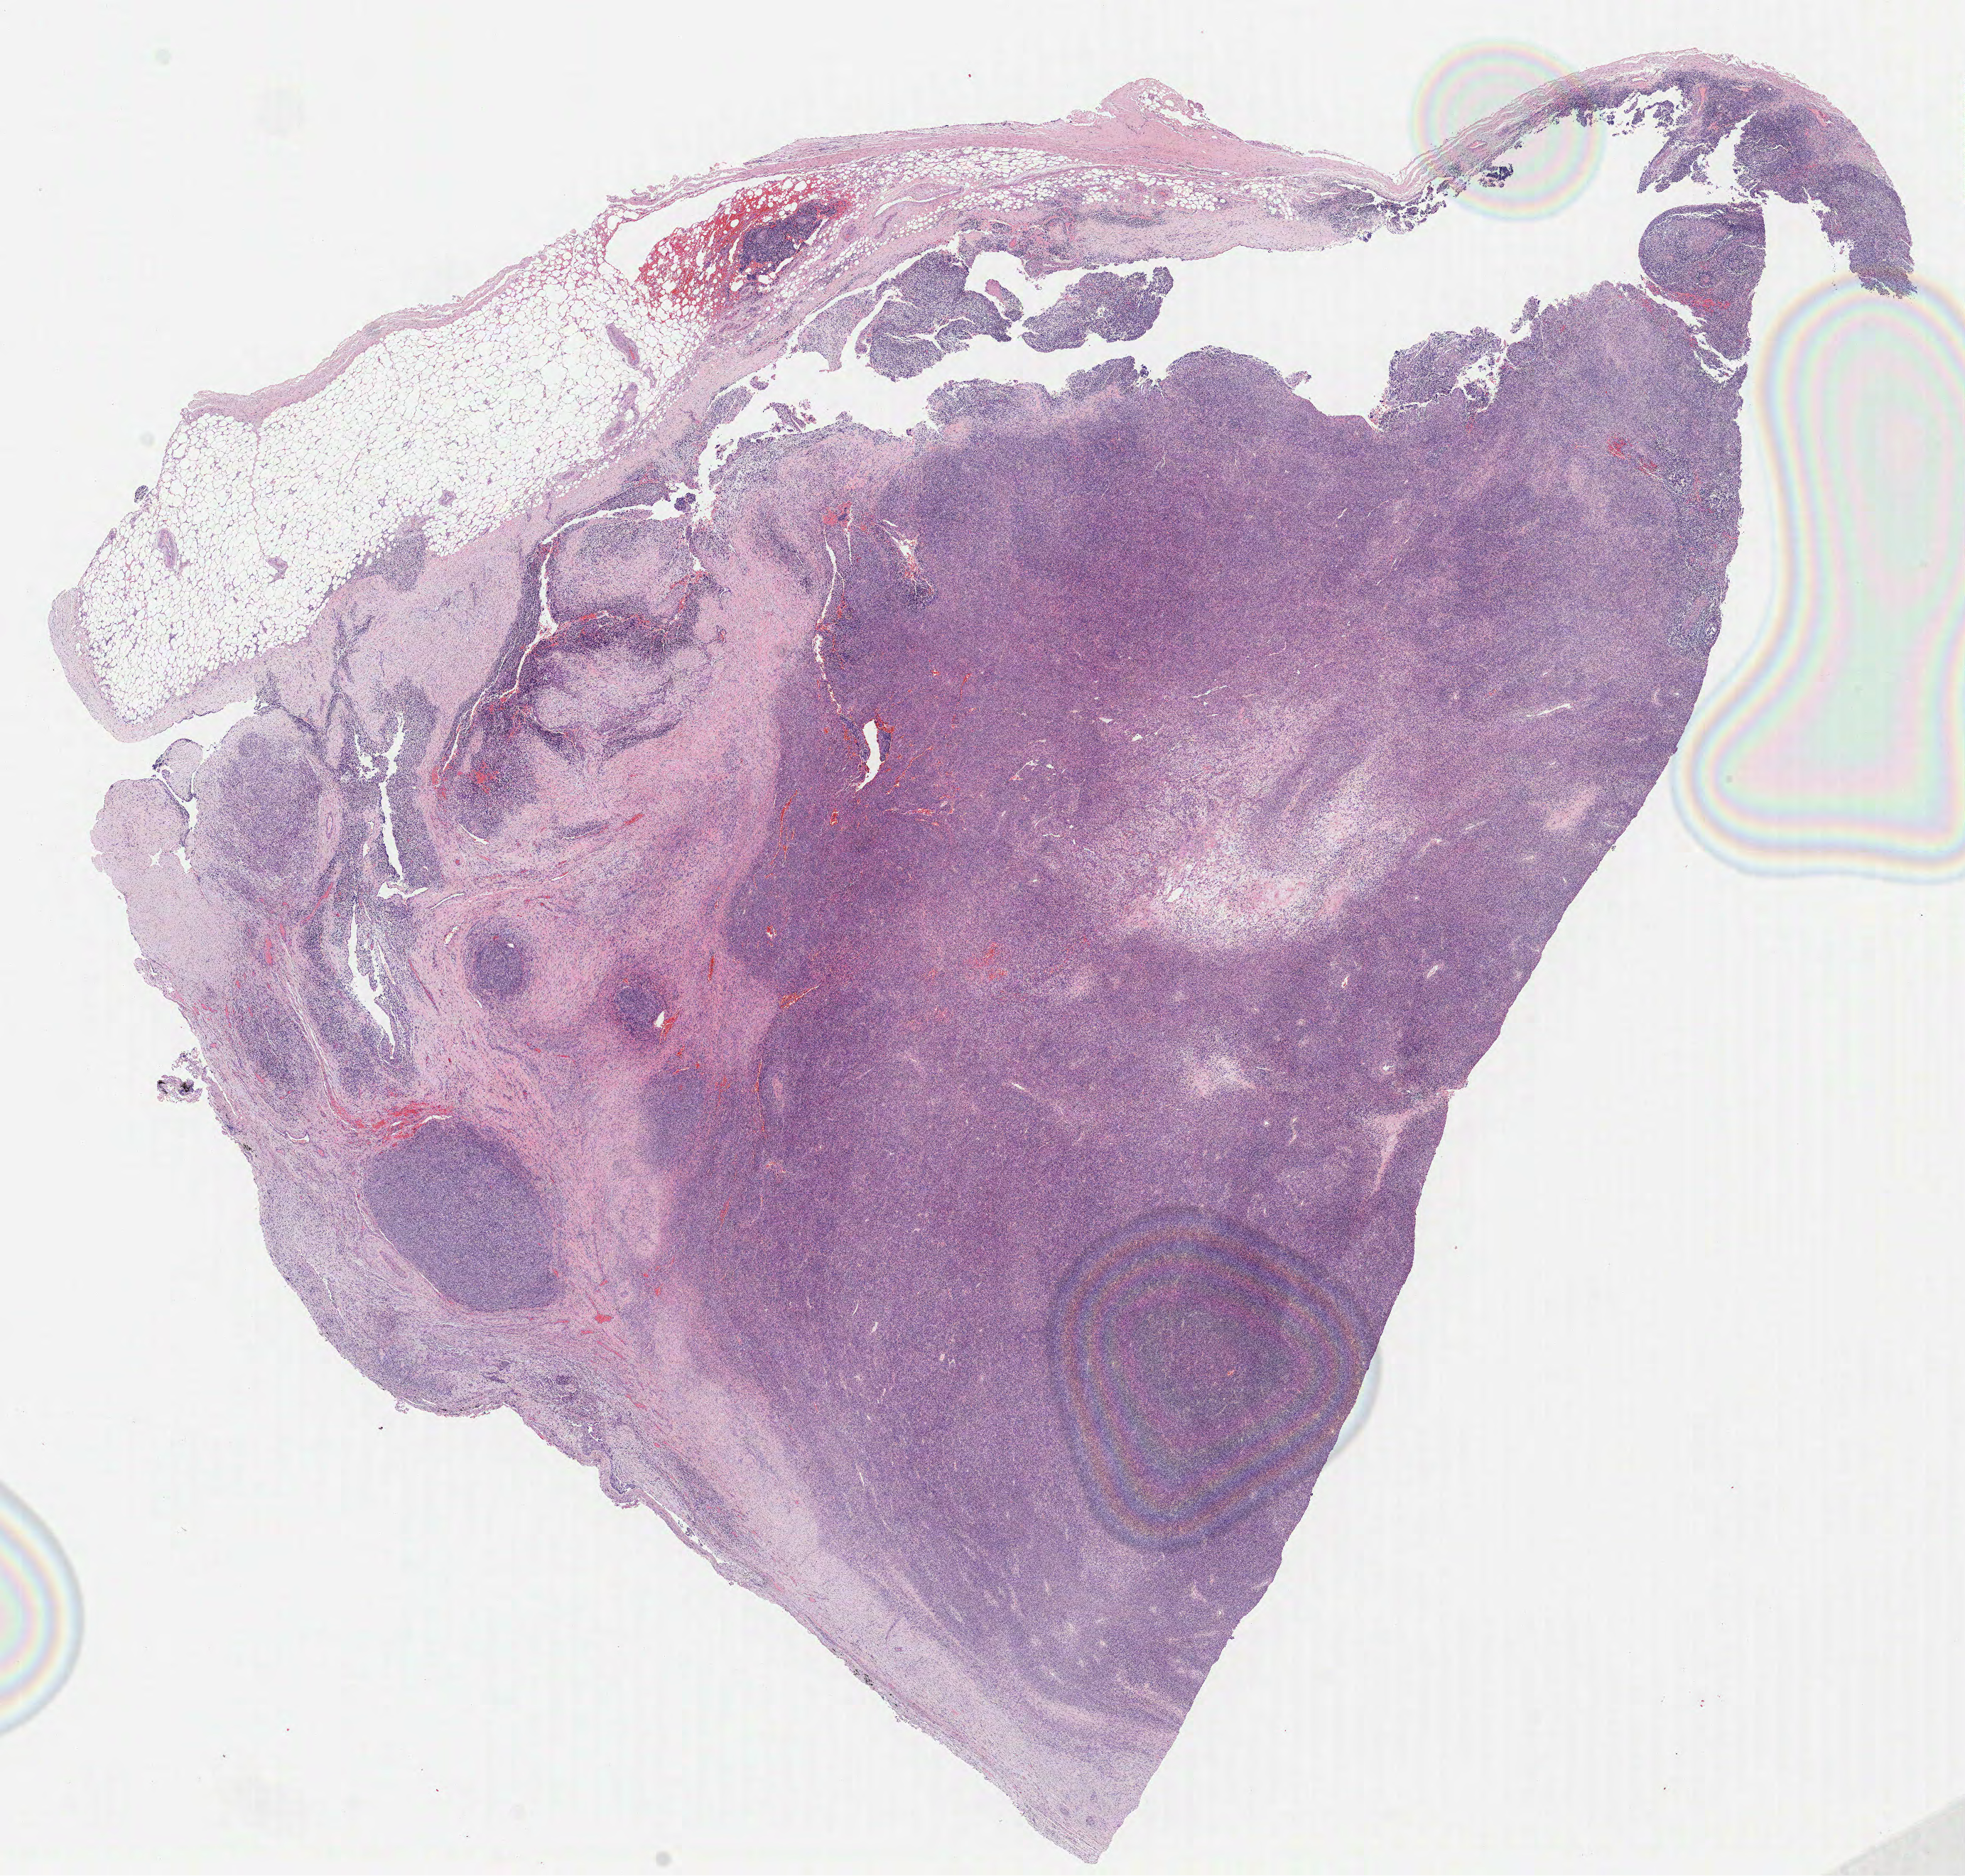
H&E-stained whole-slide image — low-resolution overview of the scanned area, about 22.1 x 21.1 mm (from a 40x scan); FFPE section; sample: primary tumour, mesothelium. Male patient; age at initial diagnosis 73 years.
TNM: T3 N0 M0. AJCC pathologic stage: III (7th edition). Diagnosis: Mesothelioma, biphasic, malignant (pleura, NOS).